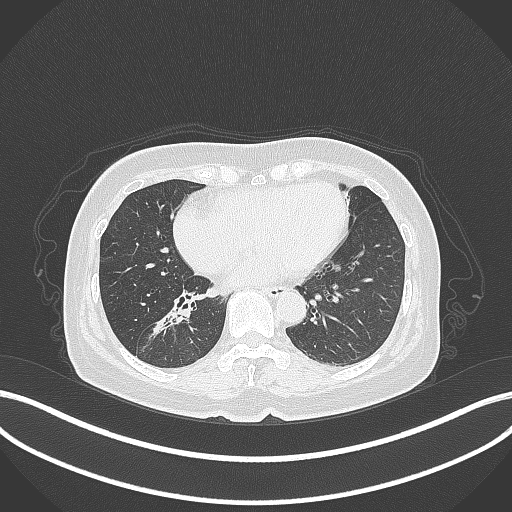
Chest CT, one axial slice. Slice 153 of 429 in the series (ordered by position). Reconstruction kernel B70f. Lung window (W 1500 / L -600 HU). 512 × 512 image matrix, field of view 400 × 400 mm. Female patient, age 67 years. From the clinical record (not read from this slice): clinical TNM (as recorded): T1c N1 M0.
Annotated regions visible in this slice (bounding box drawn by a radiologist):
- lung tumour (recorded histology: adenocarcinoma): bounding box <144,297,196,349> (left, top, right, bottom; pixels)